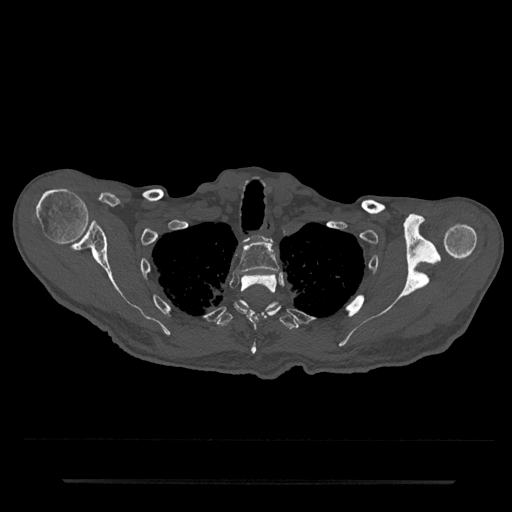
CT including the spine, one axial slice; position 657 of 797 along the scan axis; bone window (W 1800 / L 400 HU); 0.5 mm slice thickness; 512 × 512 image matrix. Patient: male, 74 years. From the clinical record (not read from this slice): primary cancer: prostate.
Outlined on this slice (semi-automatic segmentation, software-assisted and operator-edited):
- T1 vertebra: bounding box (x1, y1, x2, y2) in pixels: (257, 235, 272, 242)
- T2 vertebra: (236, 242, 279, 274)
- T3 vertebra: (234, 274, 280, 355)
- T4 vertebra: (216, 300, 300, 329)